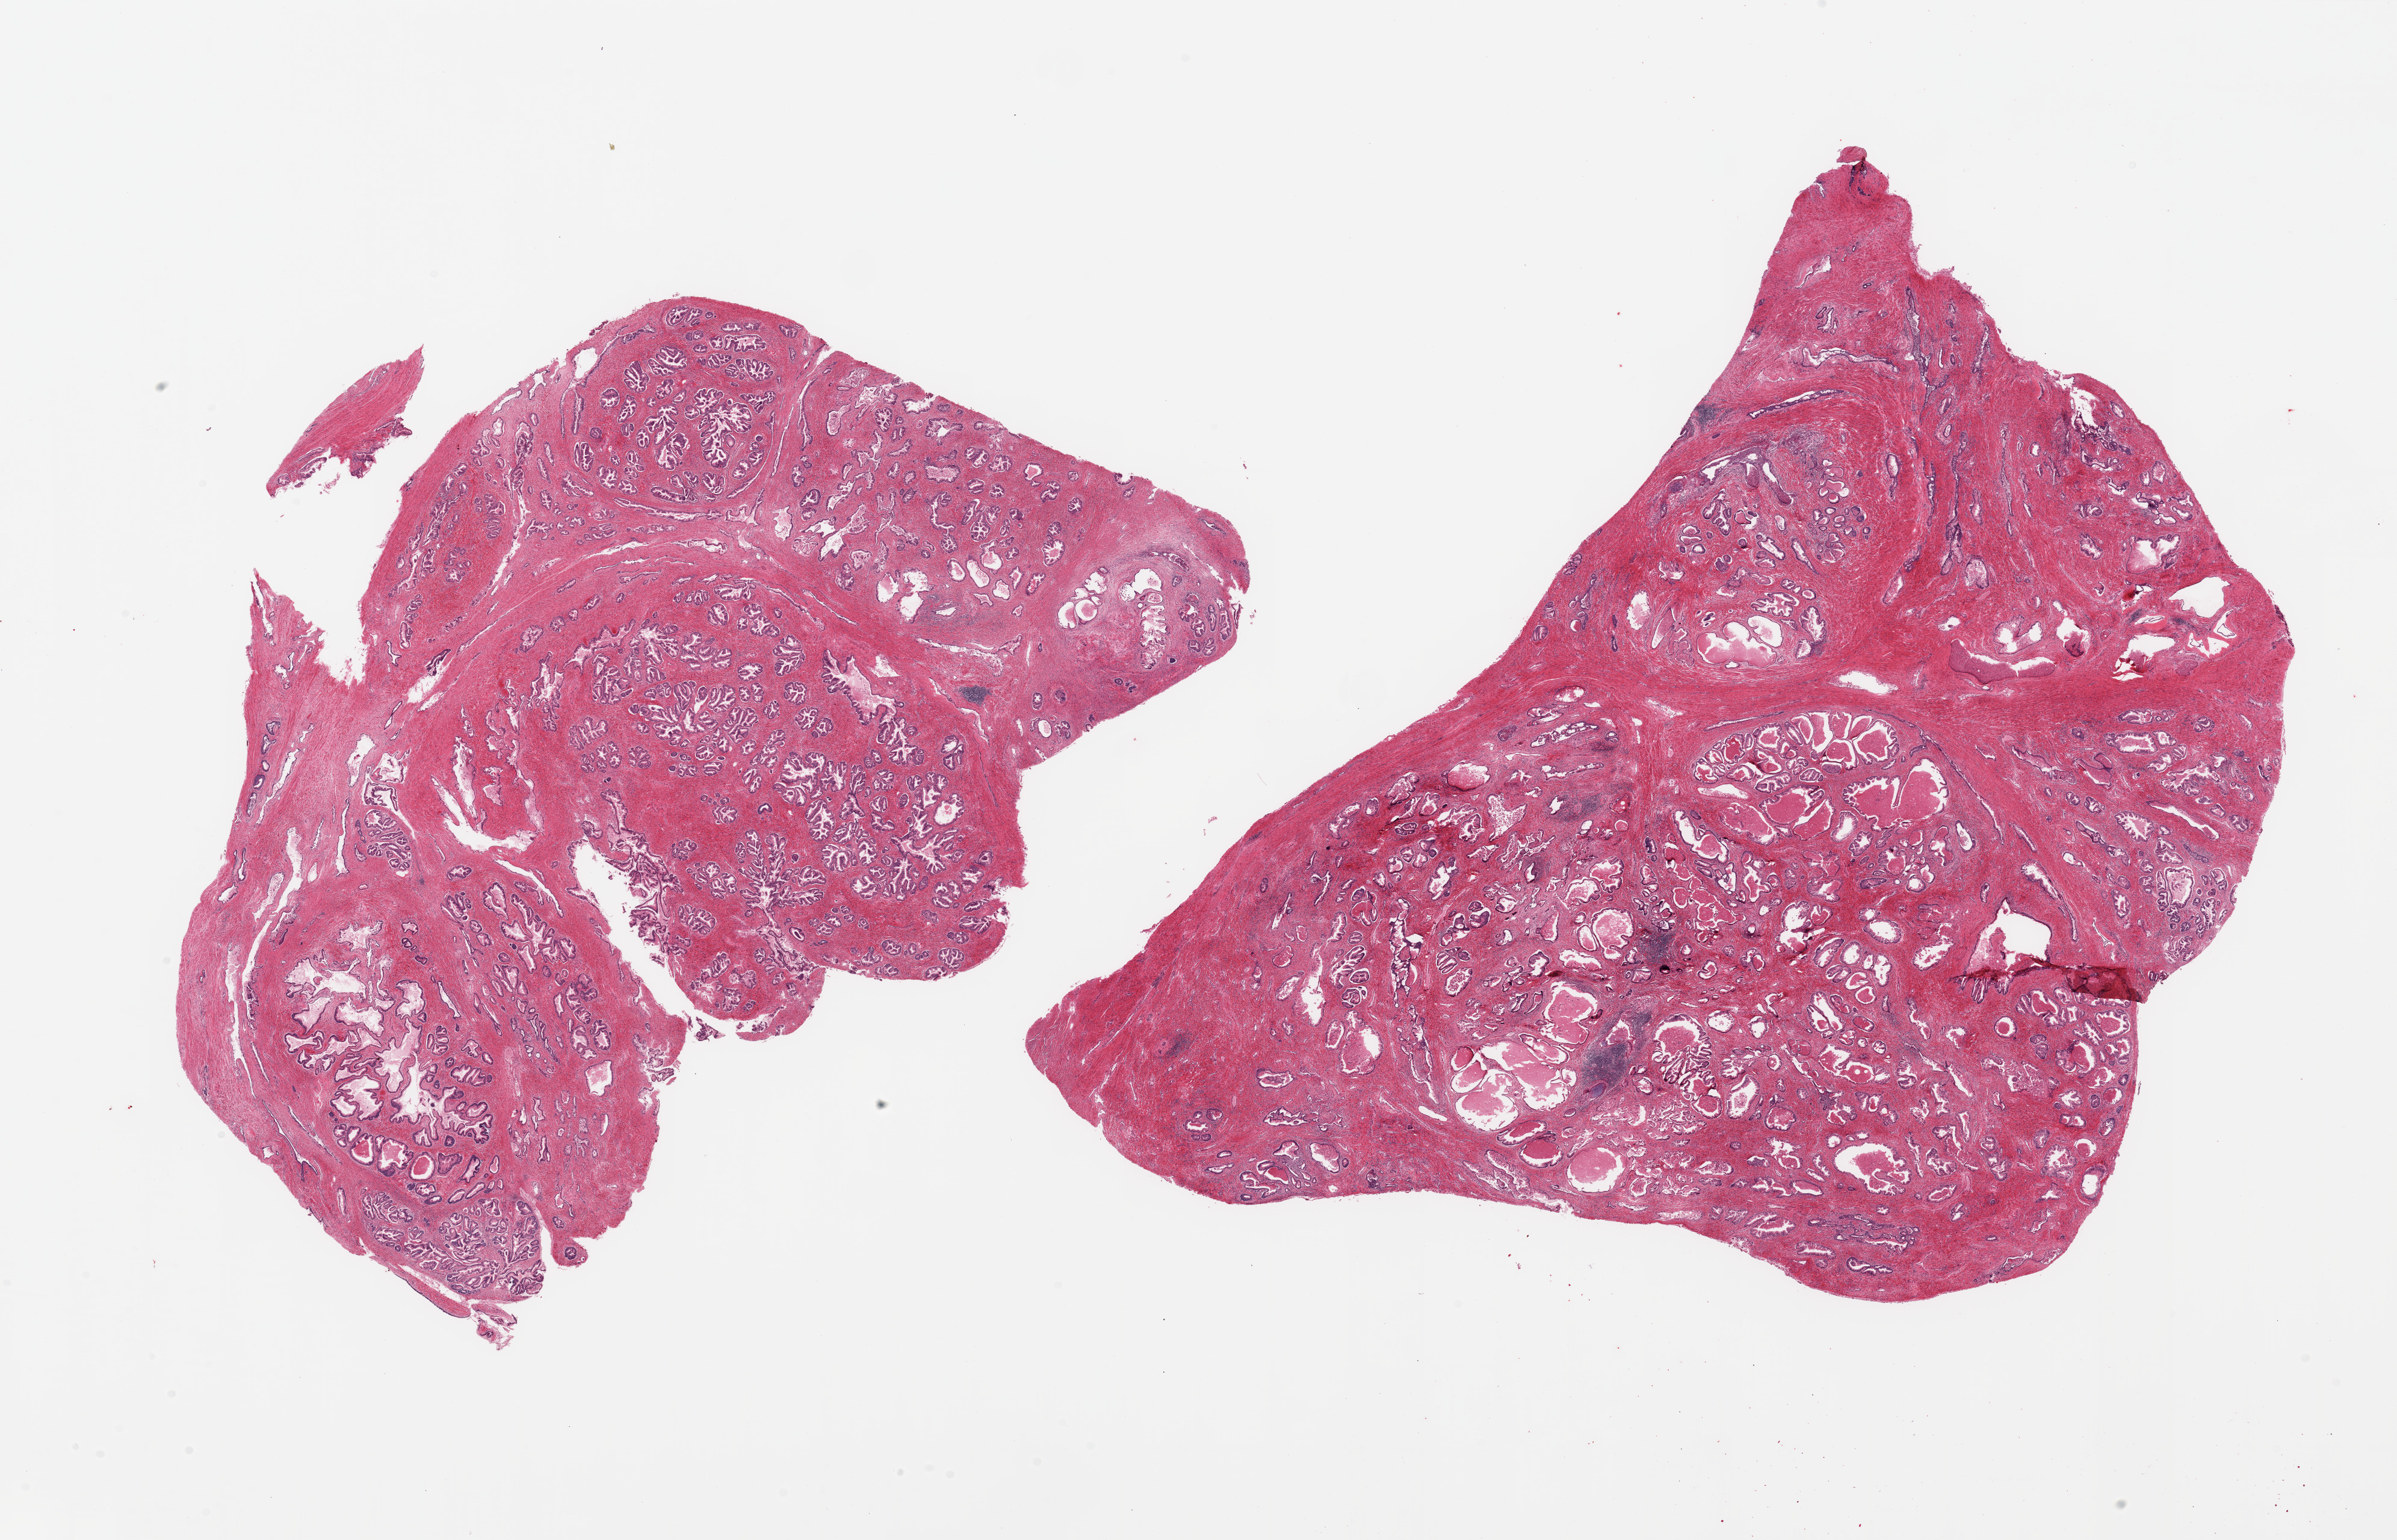
Whole-slide image, hematoxylin and eosin (H&E) stain — a low-resolution overview of the entire scanned area, about 31.5 x 20.2 mm, PAXgene-fixed, paraffin-embedded tissue, section of prostate (target tissue), donor tissue sample. Donor sex: male.
Review note (as recorded): 2 pieces, patchy glandular/stromal hyeperplasia, patchy chronic prostatitis.